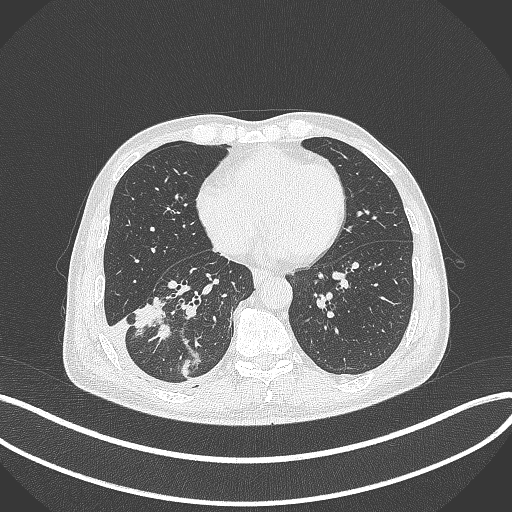
Chest CT, one axial slice; reconstruction kernel B70f; 120 kVp; lung window (W 1500 / L -600 HU); 512 × 512 image matrix. Male patient, age 64 years. From the clinical record (not read from this slice): clinical TNM (as recorded): T3 N0 M0.
Outlined on this slice (rectangle marked by the reading radiologist):
- lung tumour (recorded histology: adenocarcinoma): bounding box [x1, y1, x2, y2] px = [123, 291, 169, 333]